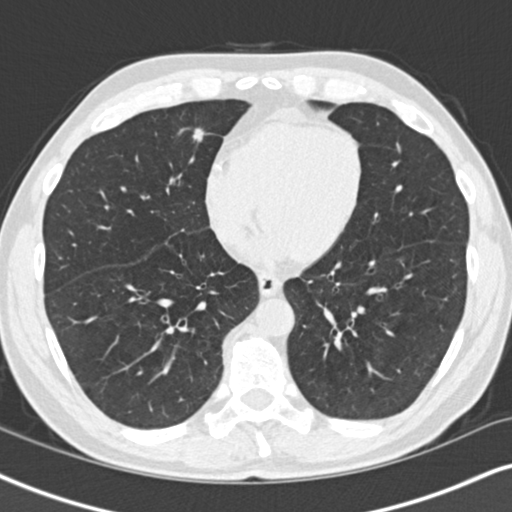
Low-dose screening chest CT, one axial slice. Position 43 of 148 along the scan axis. Reconstruction kernel B30f. Lung window (W 1500 / L -600 HU). 2 mm slice thickness. 512 × 512 image matrix, field of view 328 × 328 mm.
Outlined on this slice (expert manual segmentation):
- lesion 1 (tumor, middle lobe of right lung): bounding box (x1, y1, x2, y2) in pixels: (193, 128, 206, 142)